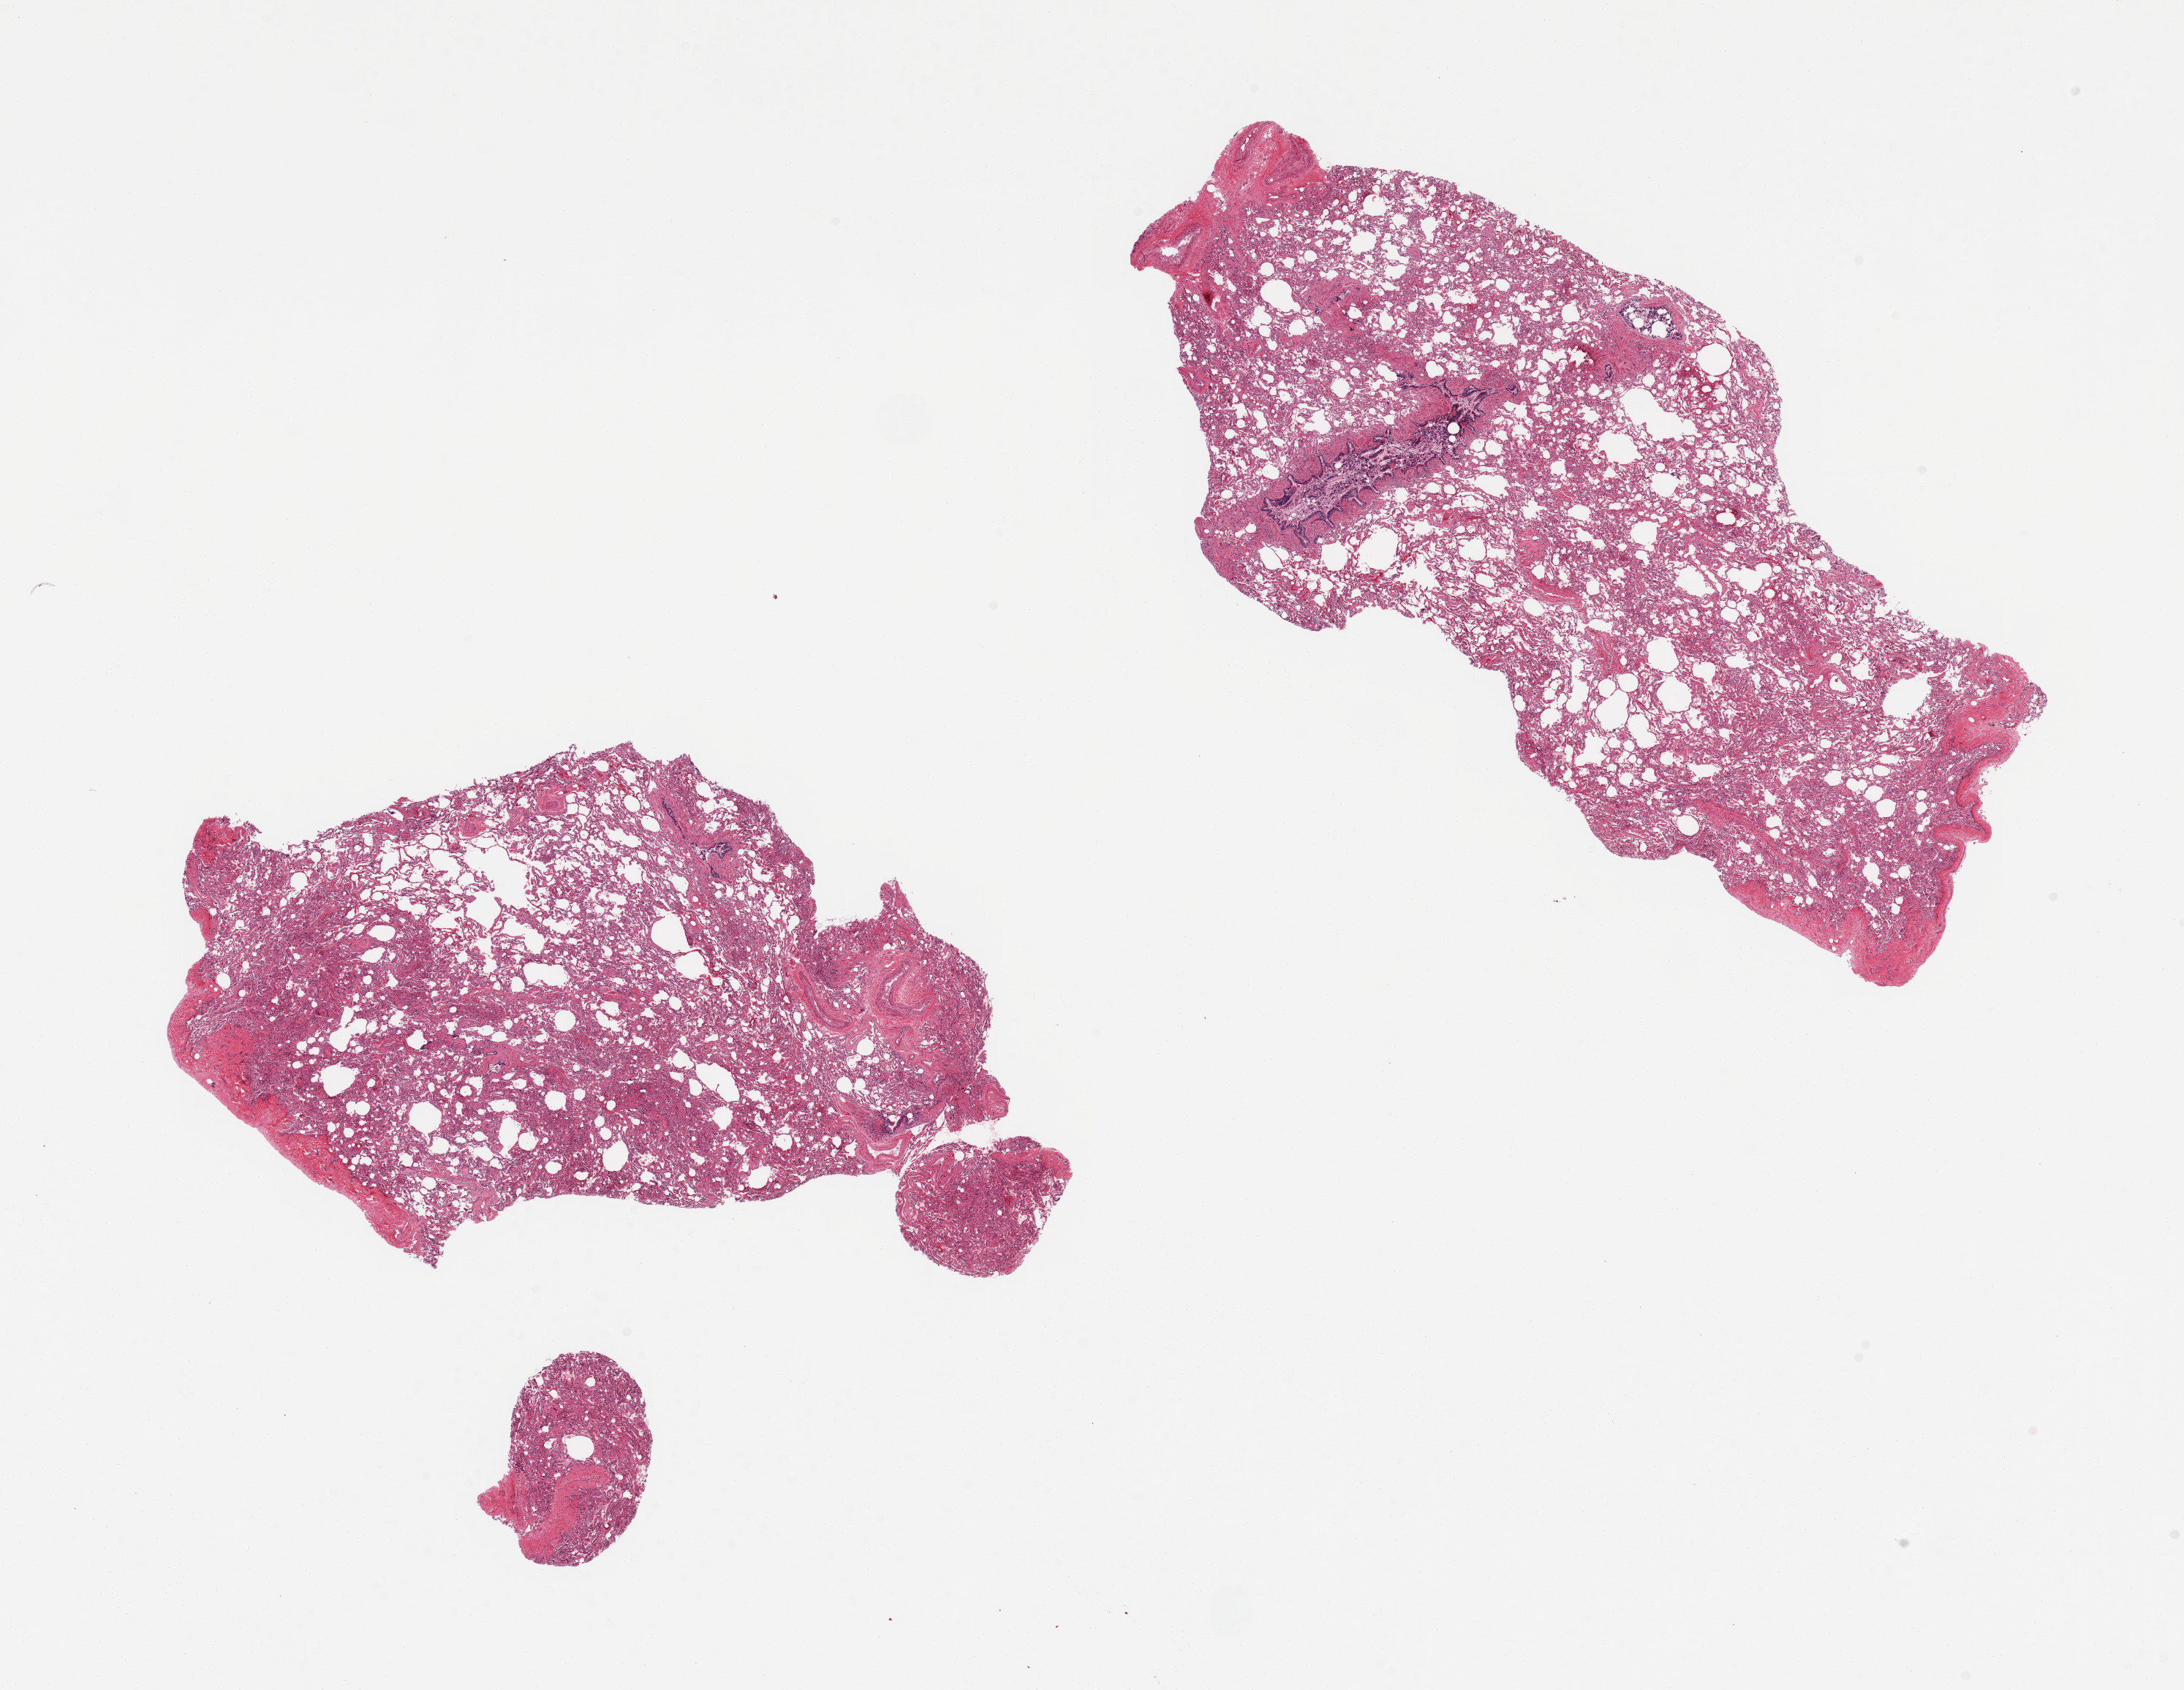
Whole-slide image, haematoxylin and eosin stain, brightfield, shown as a low-resolution overview of the whole scanned area (about 23.6 x 18.3 mm, acquisition: 20x scan), PAXgene-fixed, paraffin-embedded tissue, sampled site (target tissue): auricular appendage, tissue donor sample. Female donor.
Review note (as recorded): 2 pieces, lung, not atrial appendage.